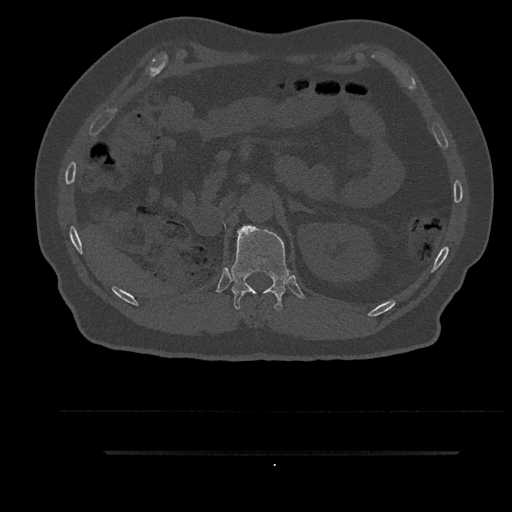
CT including the spine, one axial slice. Position 247 of 797 along the scan axis. Reconstruction kernel Br40s/3. 120 kVp. Bone window (W 1800 / L 400 HU). 0.5 mm slice thickness. 512 × 512 image matrix. Patient: male, 63 years. Case-level facts recorded for this patient, not image findings: primary cancer: renal; vertebrae with lytic lesions (as recorded): T8.
Structures marked on this image (semi-automatically segmented with operator editing):
- T12 vertebra: bounding box <229,225,291,311> (left, top, right, bottom; pixels)